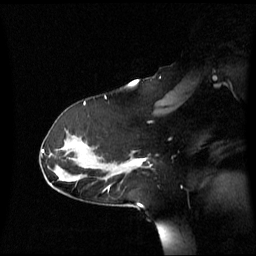
Breast MRI (dynamic contrast-enhanced), one sagittal slice; slice 40 of 60 in the series (ordered by position); dynamic contrast-enhanced series, image 2 of 3 at this slice position (ordered by acquisition); 1.5 T; TE 4.2 ms, TR 8.4 ms; 2.6 mm slice thickness; 256 × 256 image matrix. Female patient, age 39 years. Case-level facts recorded for this patient, not image findings: setting: breast cancer imaged before/during neoadjuvant chemotherapy; receptor status: triple-negative.
Annotated regions visible in this slice (semi-automatic segmentation, software-assisted and operator-edited):
- analysis volume of interest (the breast-tissue region the enhancement analysis was run in; not a lesion): bounding box <117,151,152,175> (left, top, right, bottom; pixels)
- tumour enhancement mask (voxels above the 70 % enhancement threshold inside the analysis volume of interest): <133,158,151,167>